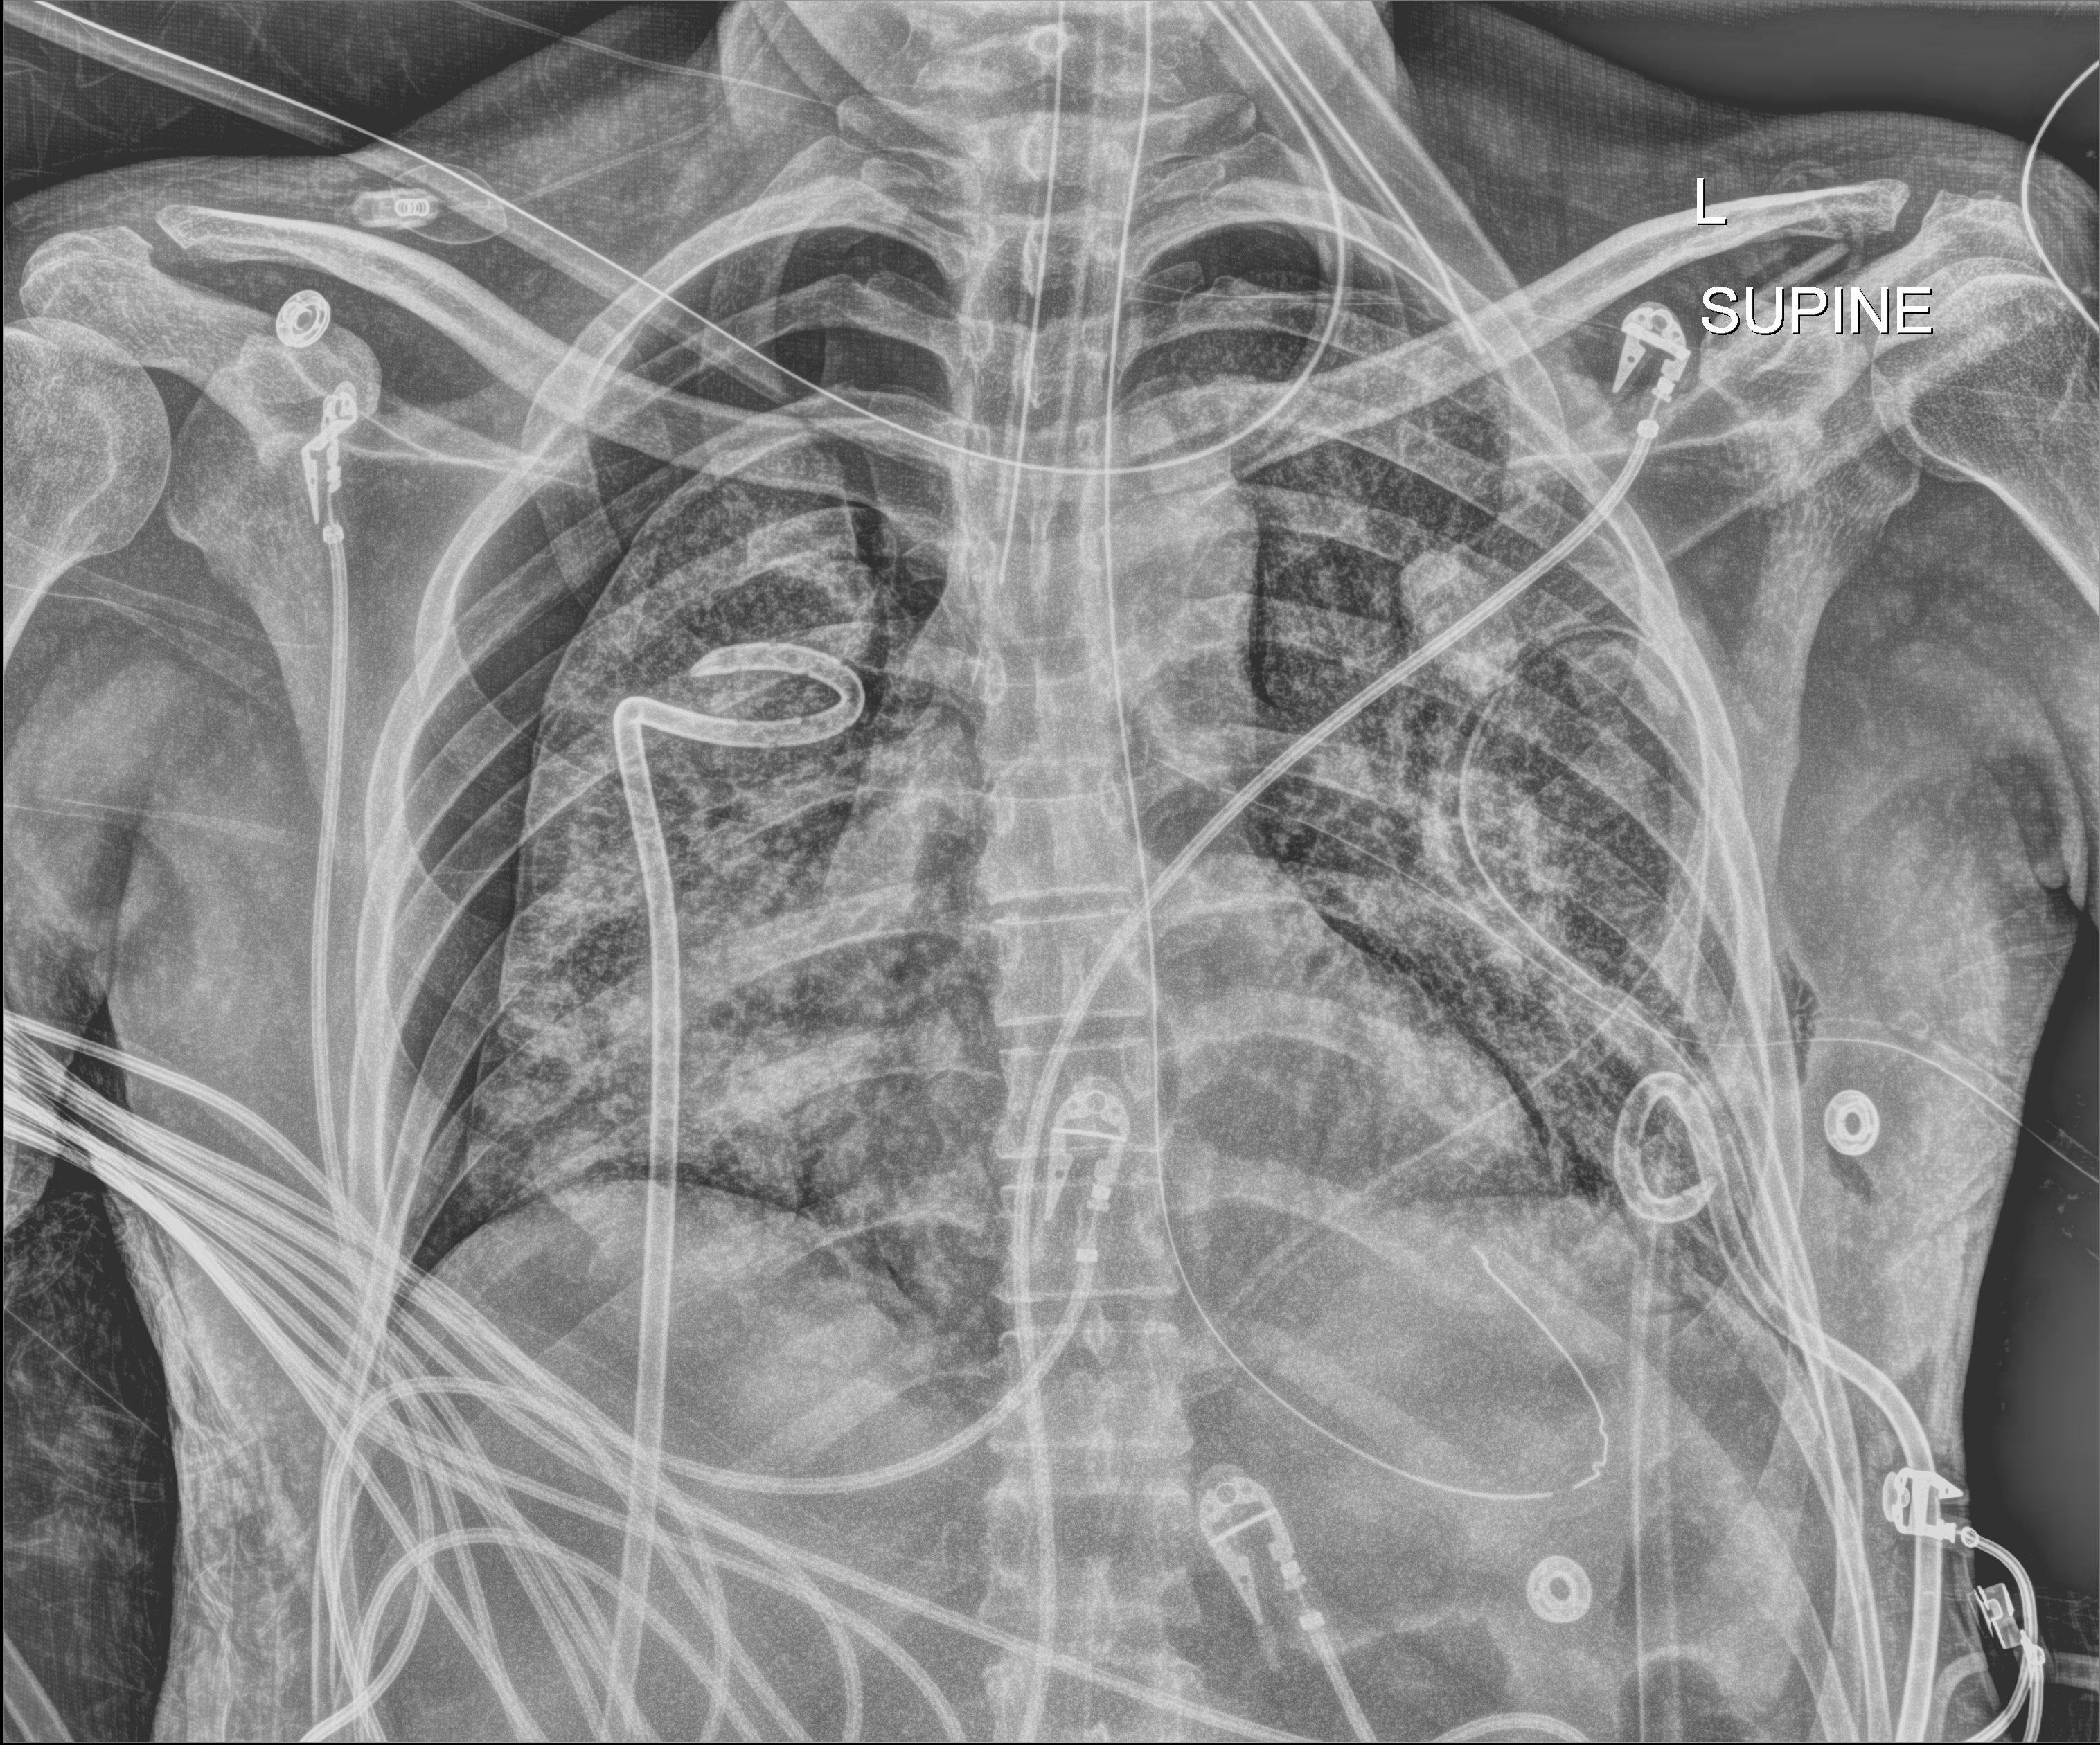
Chest radiograph; anteroposterior (AP) projection. Patient hospitalised with COVID-19, aged 18–59 years.
From the hospital-stay record, not from the radiograph (when in the stay this image was taken is not recorded): mechanically ventilated during this hospital stay: yes; other chronic lung disease (admission record): no; length of hospital stay: 41 days.